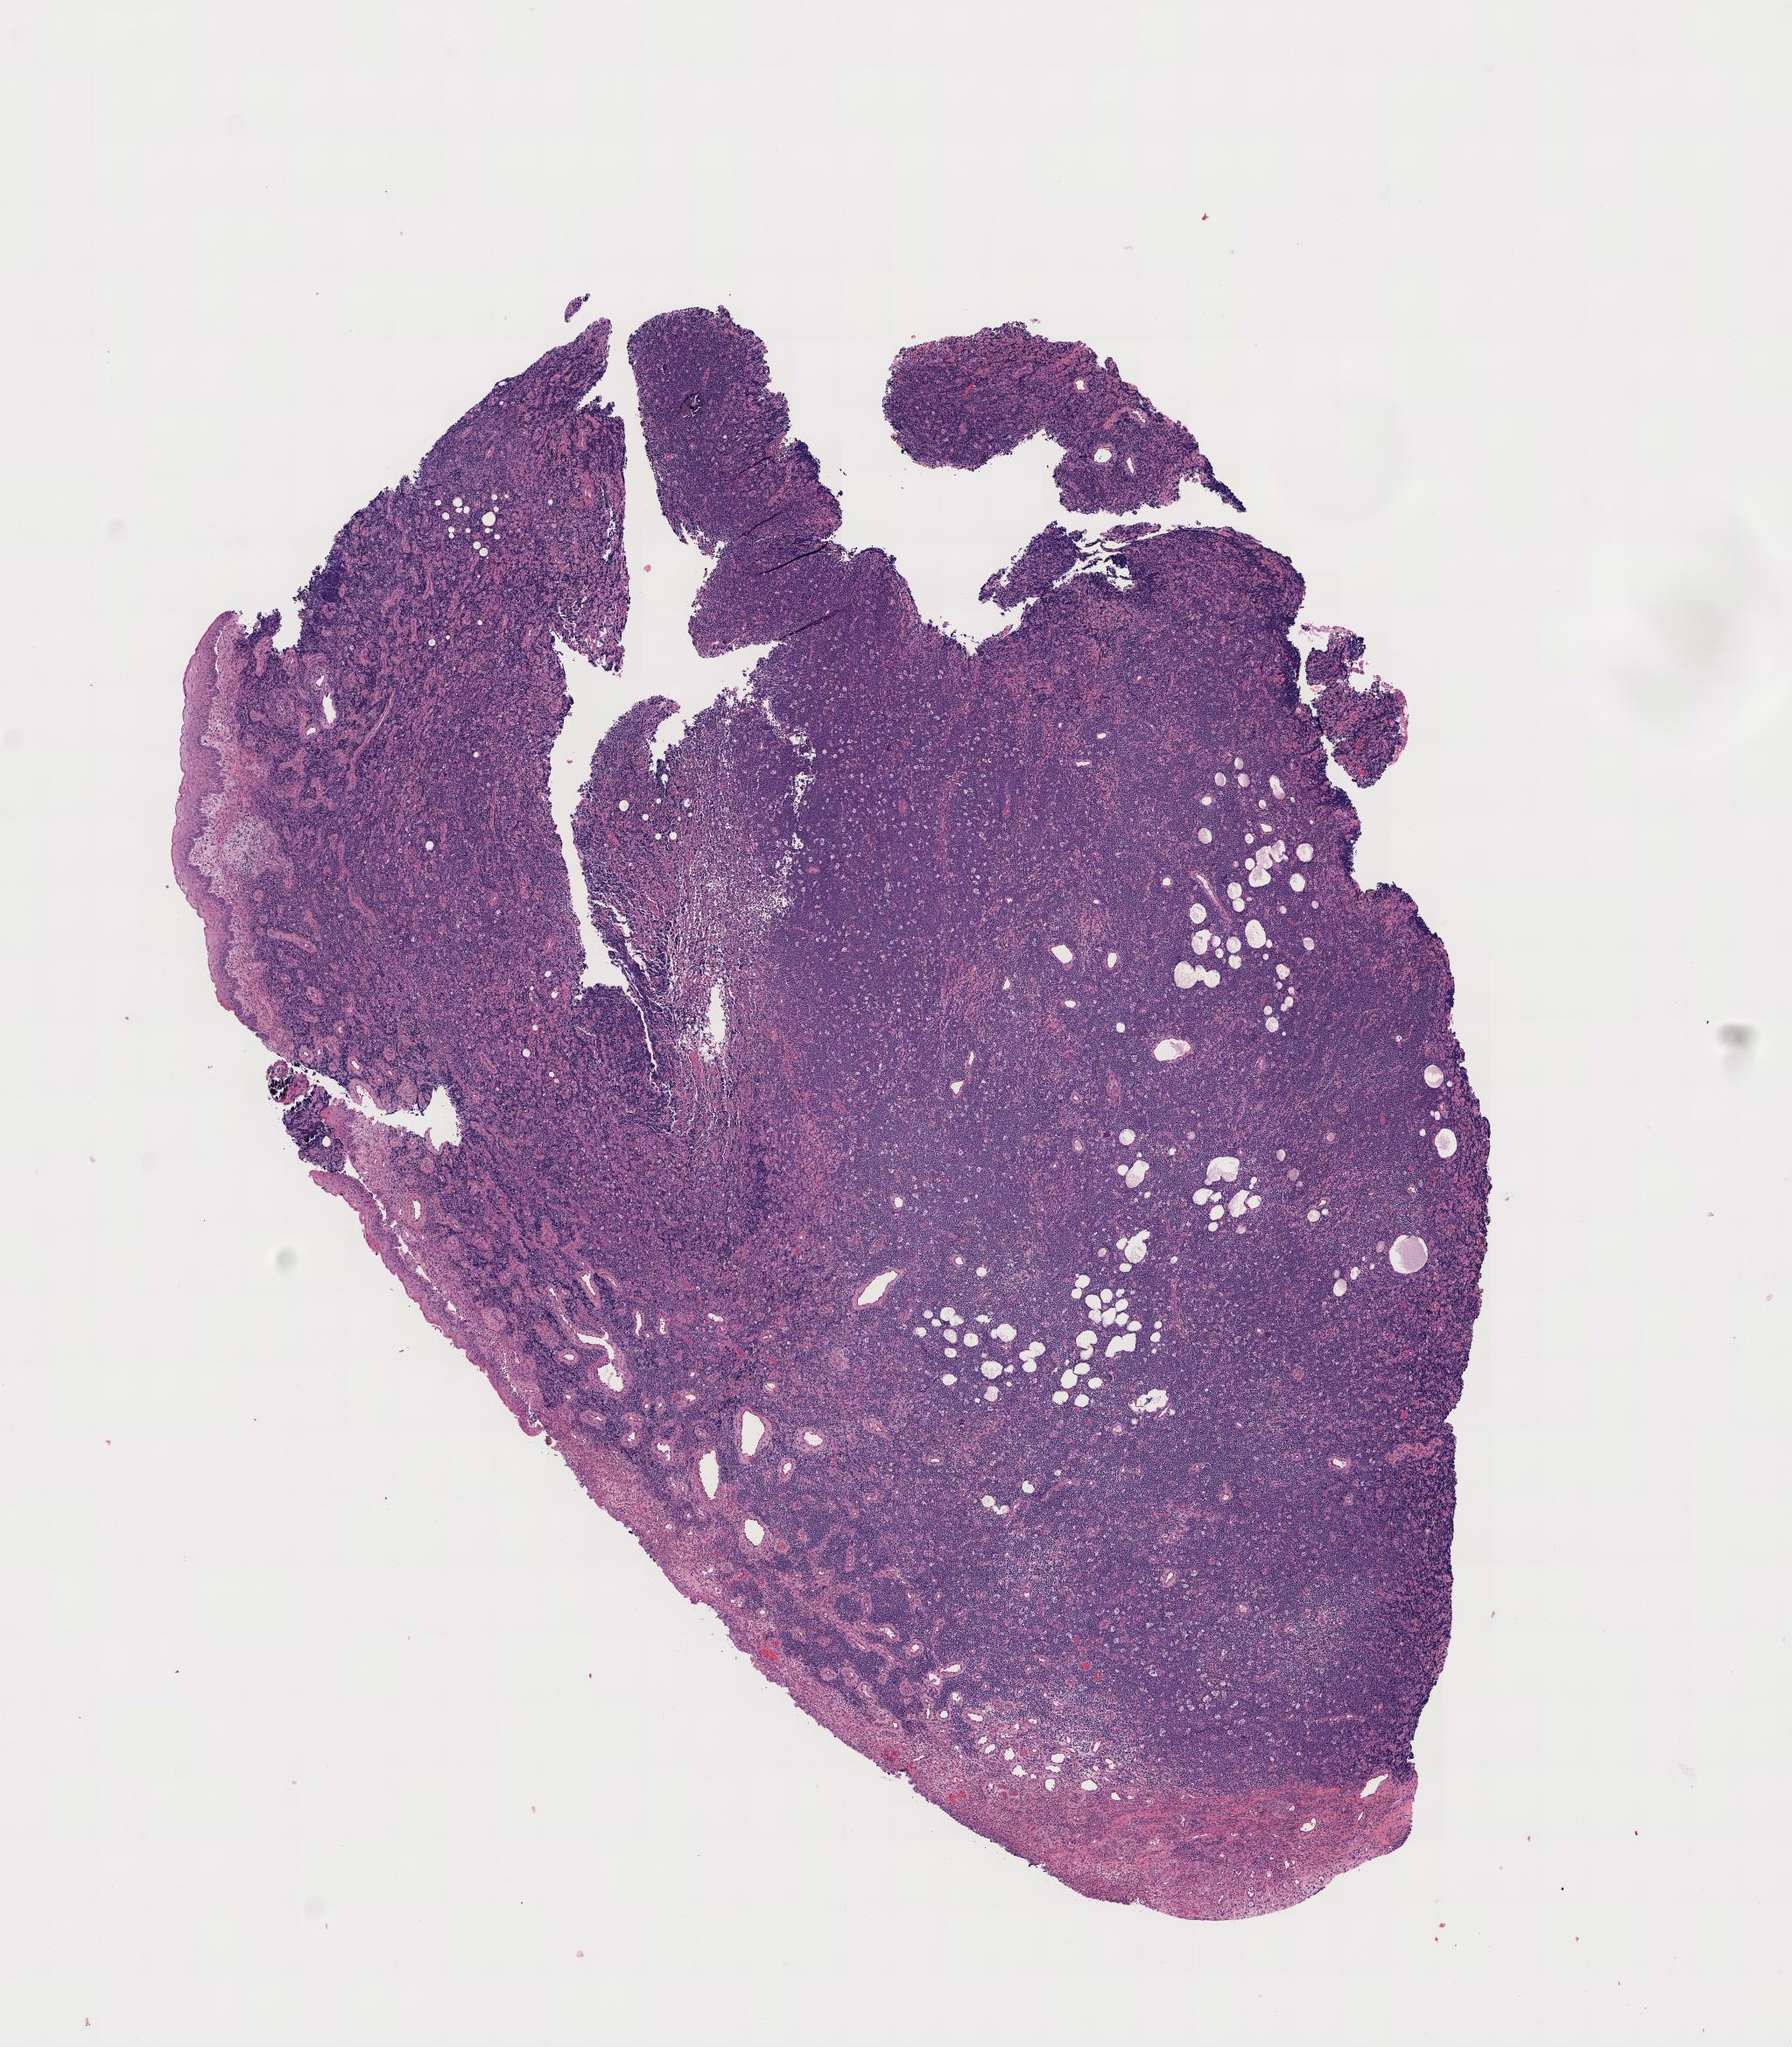
Whole-slide image, haematoxylin and eosin stain, low-resolution overview of the scanned area; tumor tissue; site: mandible. Patient: male, age 11 years.
Diagnosis: Burkitt lymphoma, NOS.